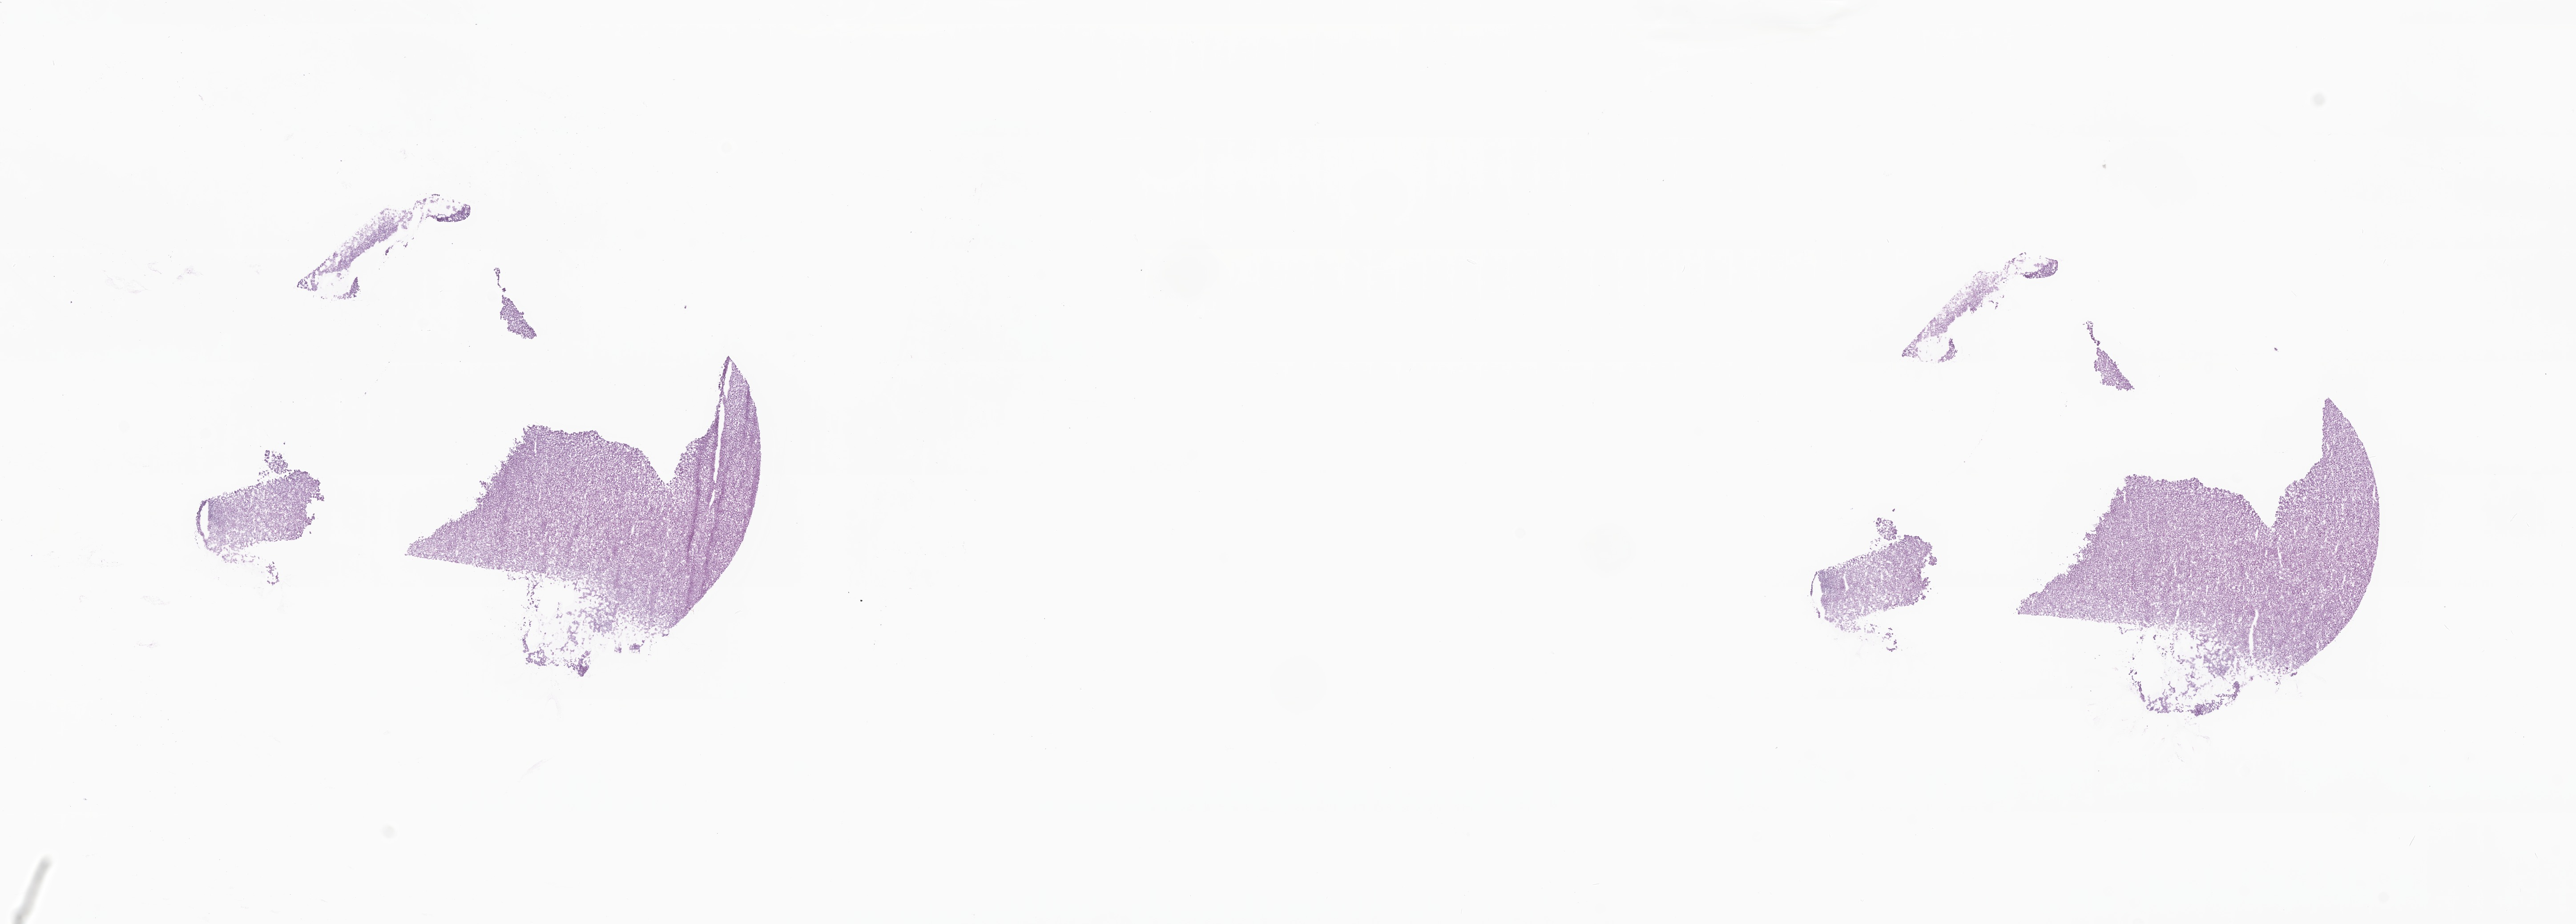
Hematoxylin and eosin (H&E) whole-slide image, shown as a low-resolution overview of the whole scanned area (about 24.4 x 8.8 mm). Frozen section (tissue freezing medium). Specimen: metastatic tumor tissue. Patient: female, age at initial diagnosis 36 years. Pathologist review of this section (percent, as recorded): tumor cells 90%, tumor nuclei 90%, stromal cells 10%, necrosis 0%, normal cells 0%. Inflammatory infiltration, as recorded: lymphocyte infiltration 0%, monocyte infiltration 0%, neutrophil infiltration 0%.
Patient diagnosis (primary): Adenocarcinoma, NOS. Section: bottom of the tissue portion.